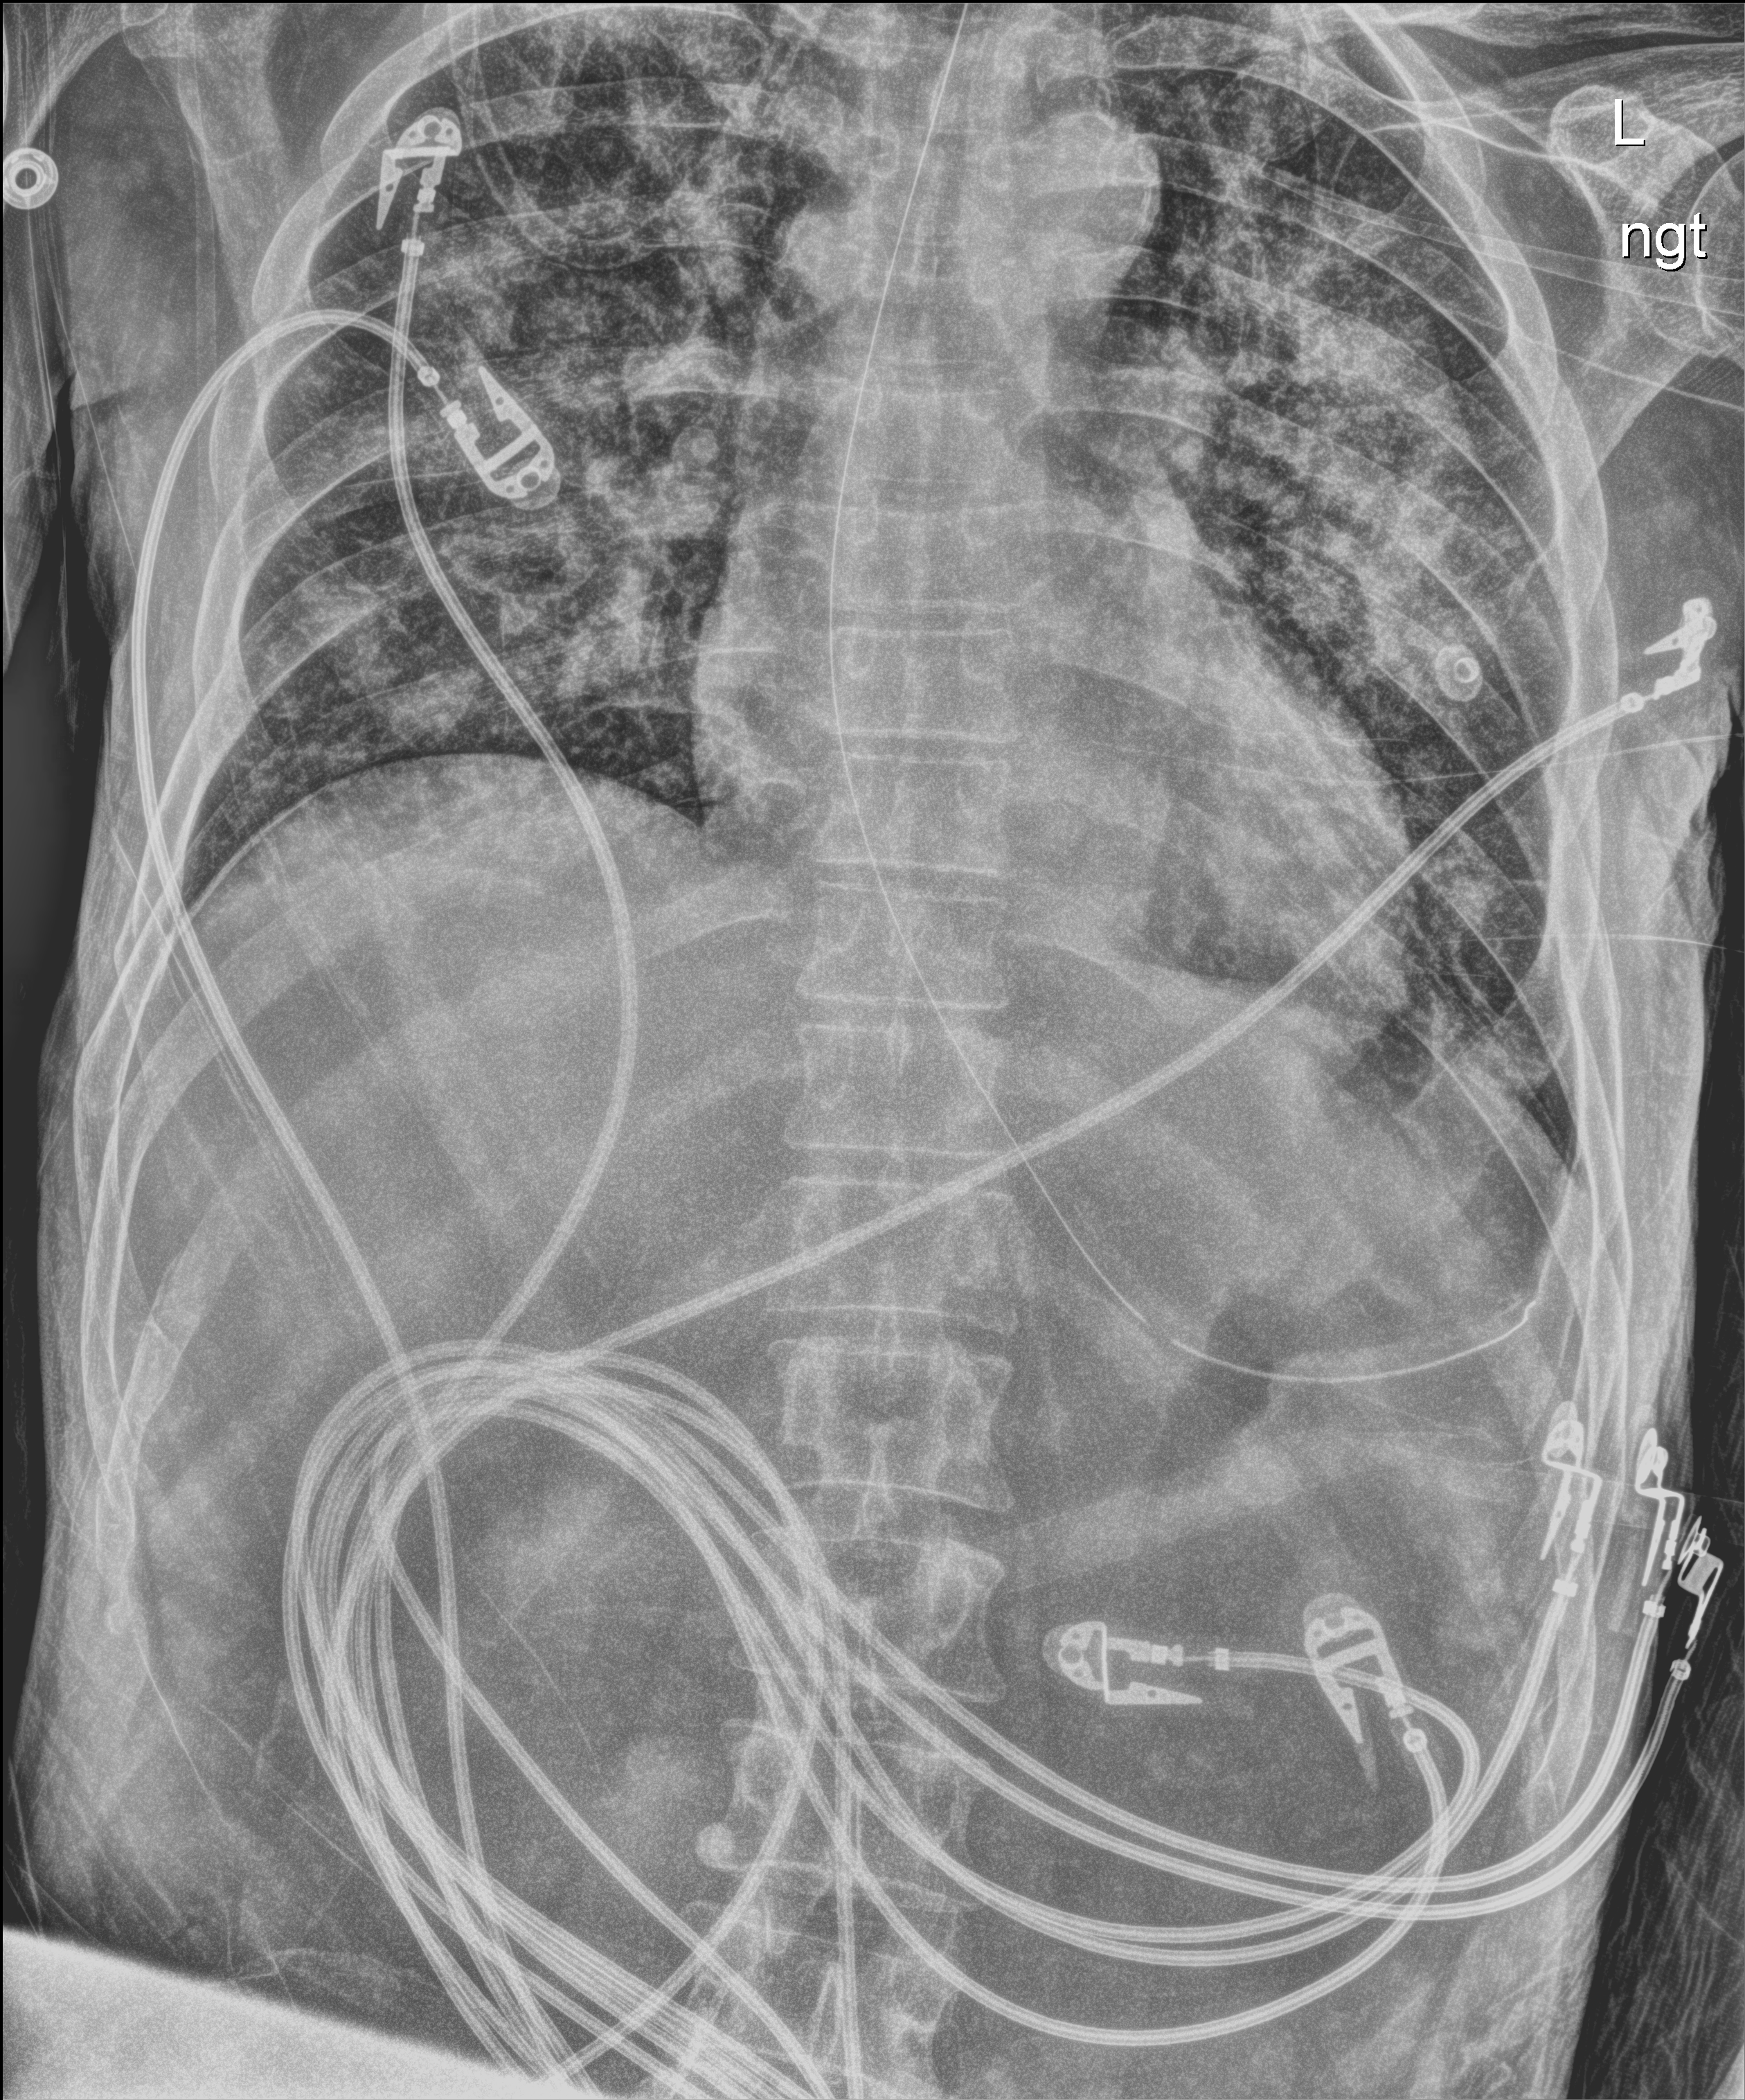
Chest X-ray (portable), anteroposterior (AP) projection. Male patient hospitalised with COVID-19, age 18–59 years.
From the hospital-stay record, not from the radiograph (when in the stay this image was taken is not recorded):
- mechanically ventilated during this hospital stay: no